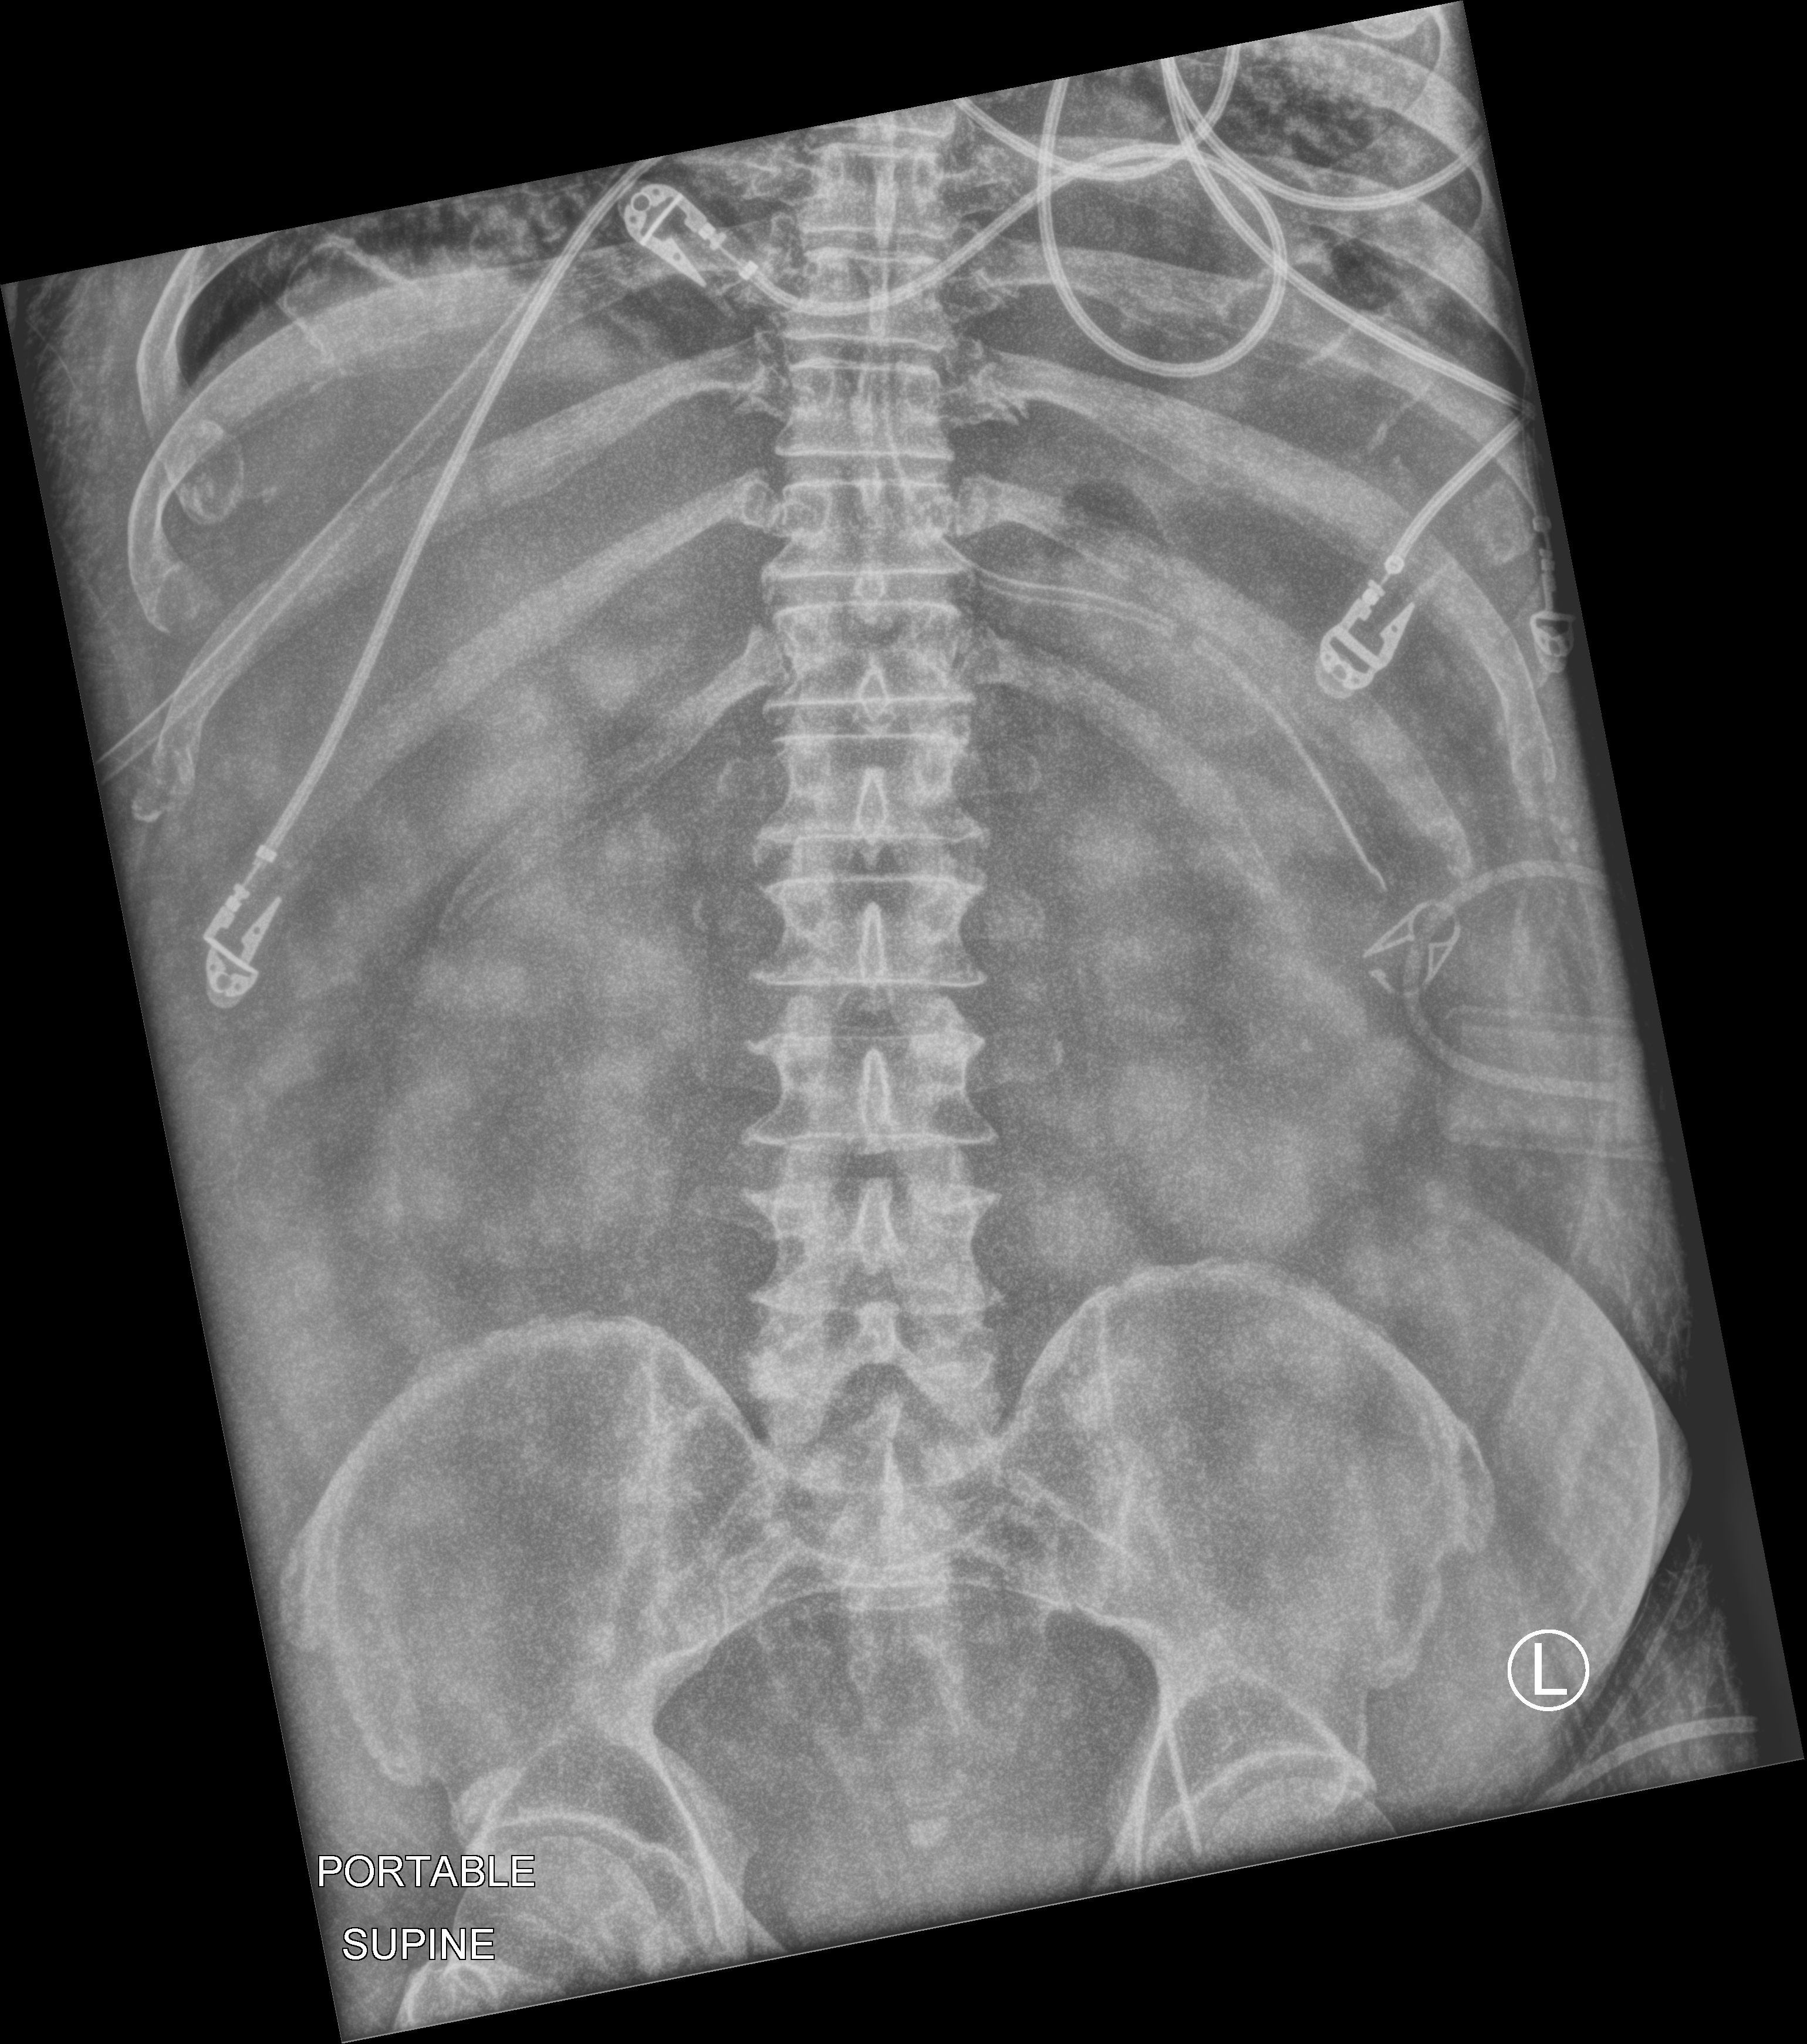
Bedside abdomen radiograph (computed radiography), anteroposterior (AP) projection. Male patient hospitalised with COVID-19, age 60–74 years.
Hospital-stay facts (about this admission, not read from this image; timing relative to this image not recorded):
- mechanically ventilated during this hospital stay: yes
- admitted to intensive care during this hospital stay: yes
- diabetes (admission record): no